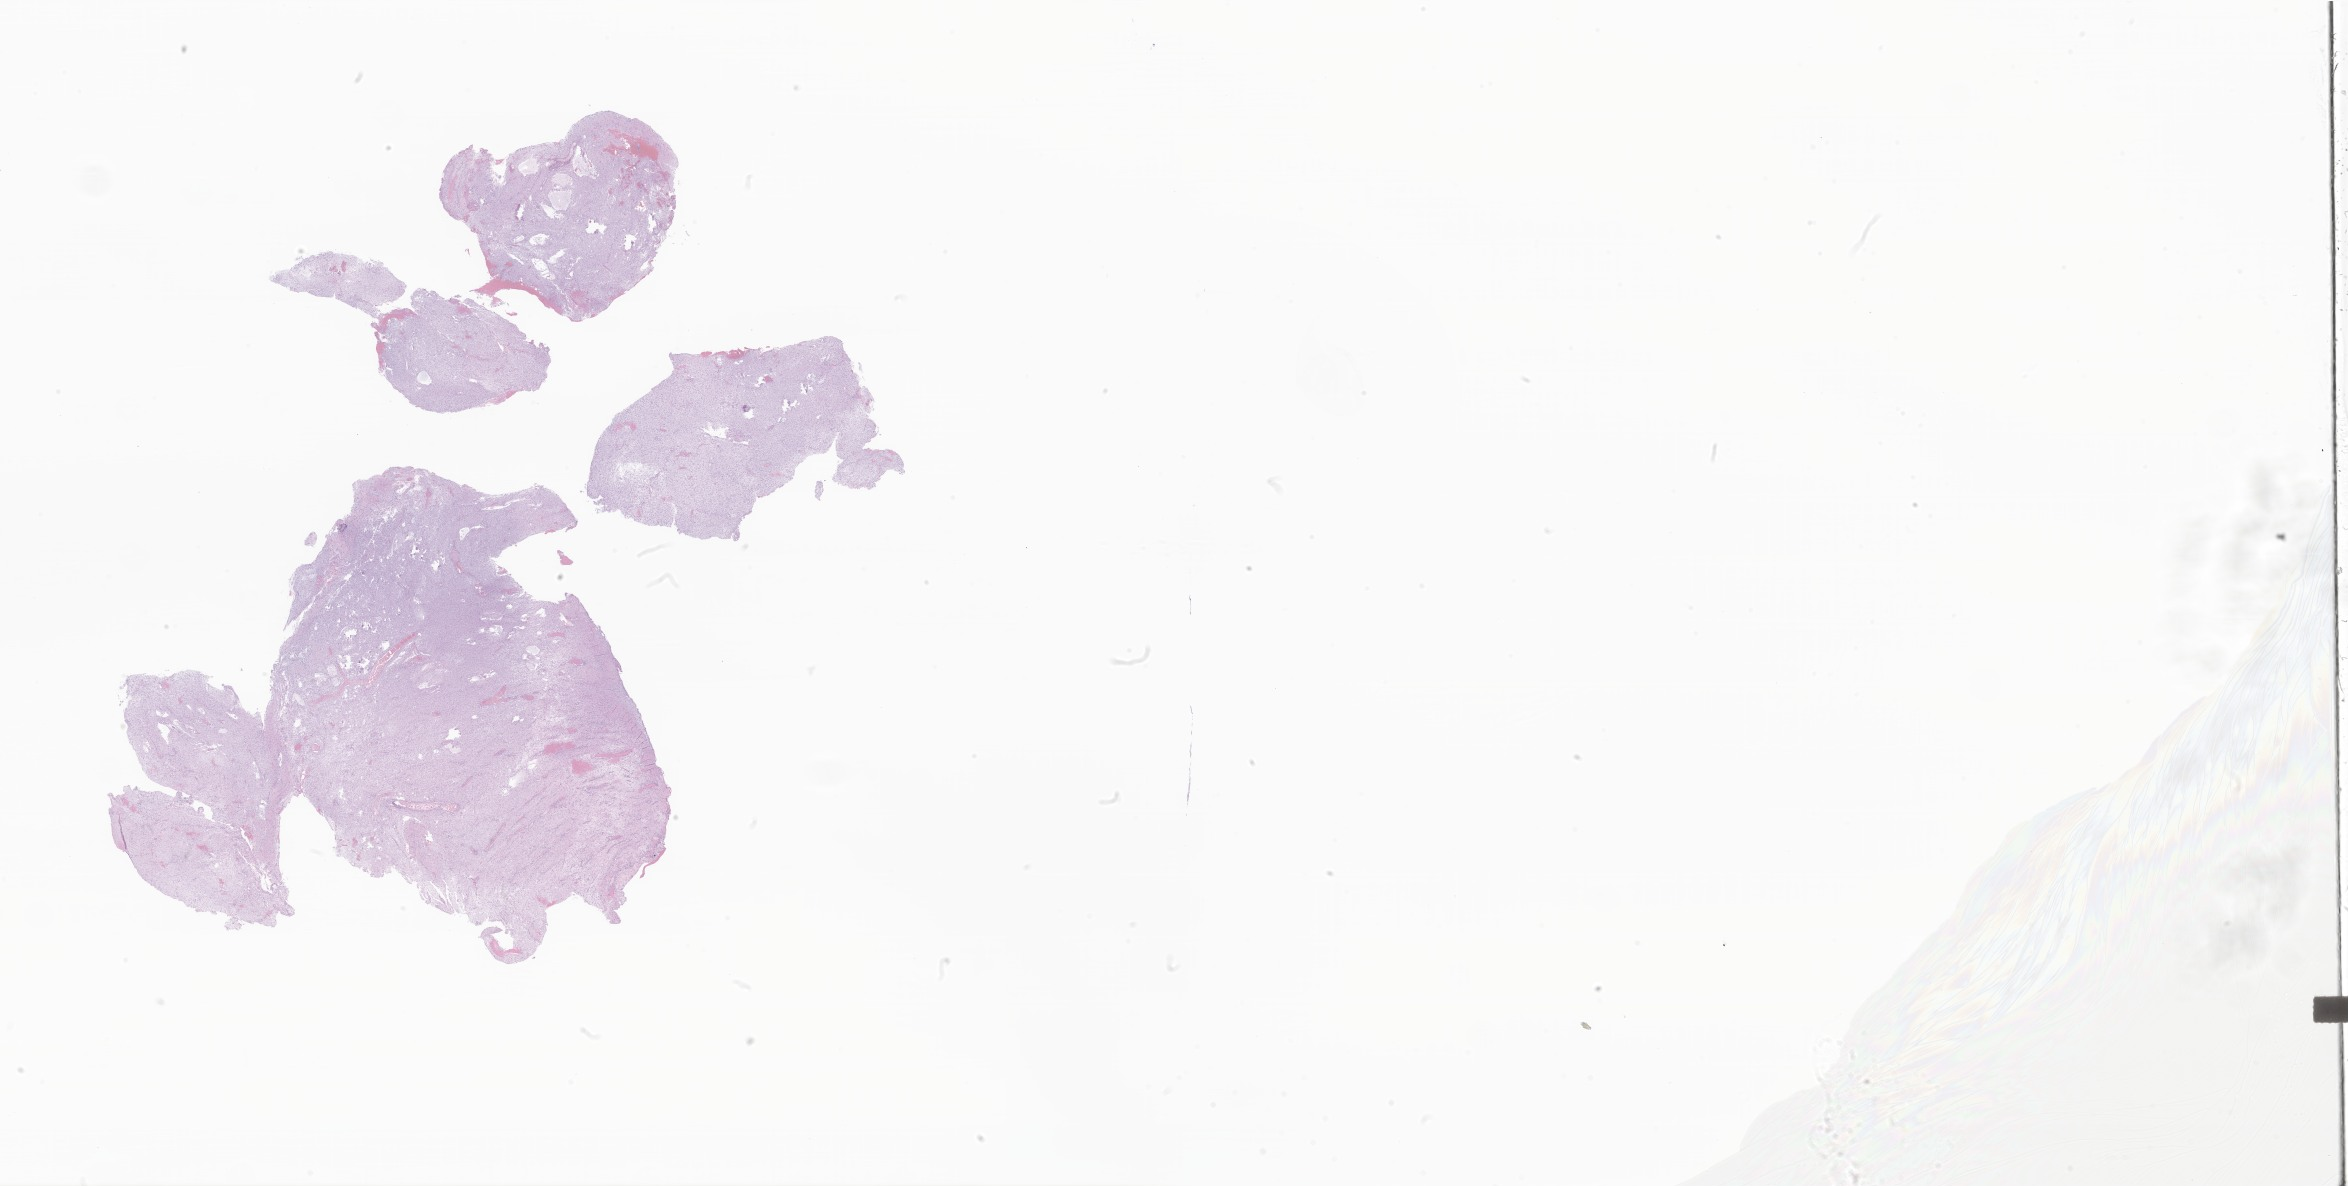
Hematoxylin and eosin (H&E) whole-slide image of tumor tissue from the occipital lobe, low-resolution overview of the scanned area, about 39.6 x 20.0 mm. Formalin-fixed paraffin-embedded section. Patient female; age 104 months.
• diagnosis: Pilocytic astrocytoma